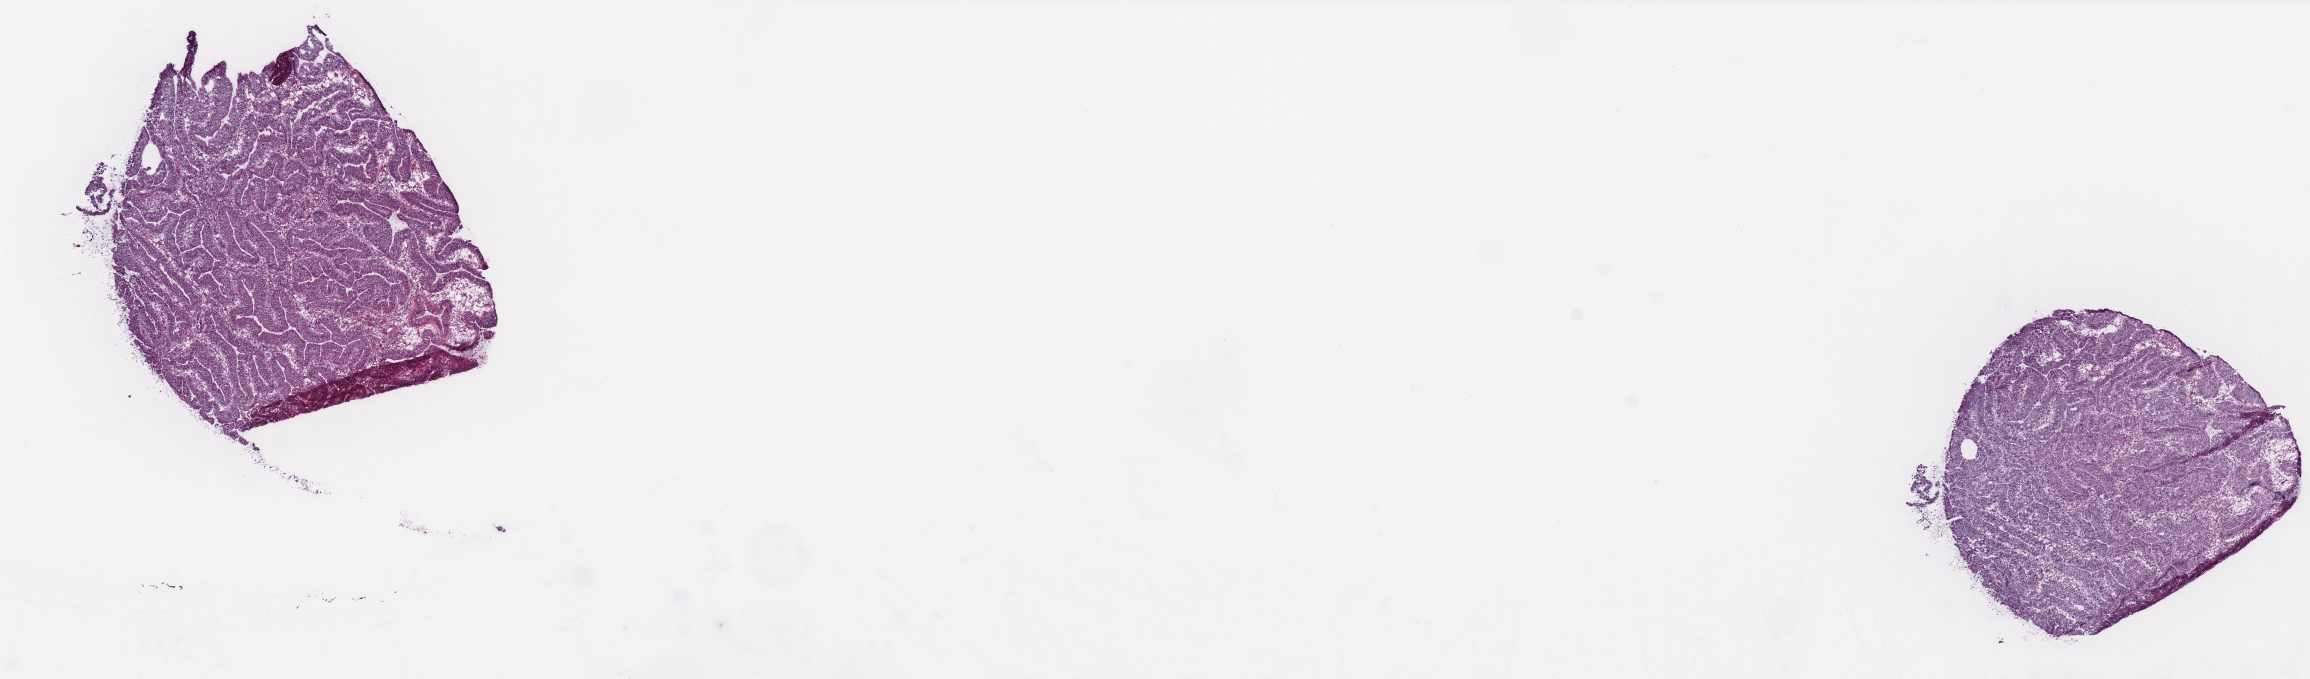
Digitized Hematoxylin and eosin (H&E) stained tissue section (whole slide) — low-resolution overview of the scanned area, about 18.5 x 5.4 mm (slide scanned at 40x). Frozen section from the top of the tissue portion. Primary tumour sample from the rectum. Male, age 77 years at initial diagnosis. Slide review estimates, as recorded: tumour cells 92%, tumour nuclei 75%, normal cells 0%, stromal cells 5%, necrosis 3%. Inflammatory infiltration, as recorded: lymphocyte infiltration 12%, monocyte infiltration 2%, neutrophil infiltration 3%.
Histologic diagnosis: Adenocarcinoma, NOS. AJCC pathologic stage: I. Lymph nodes positive (case pathology): 0 of 15 examined.